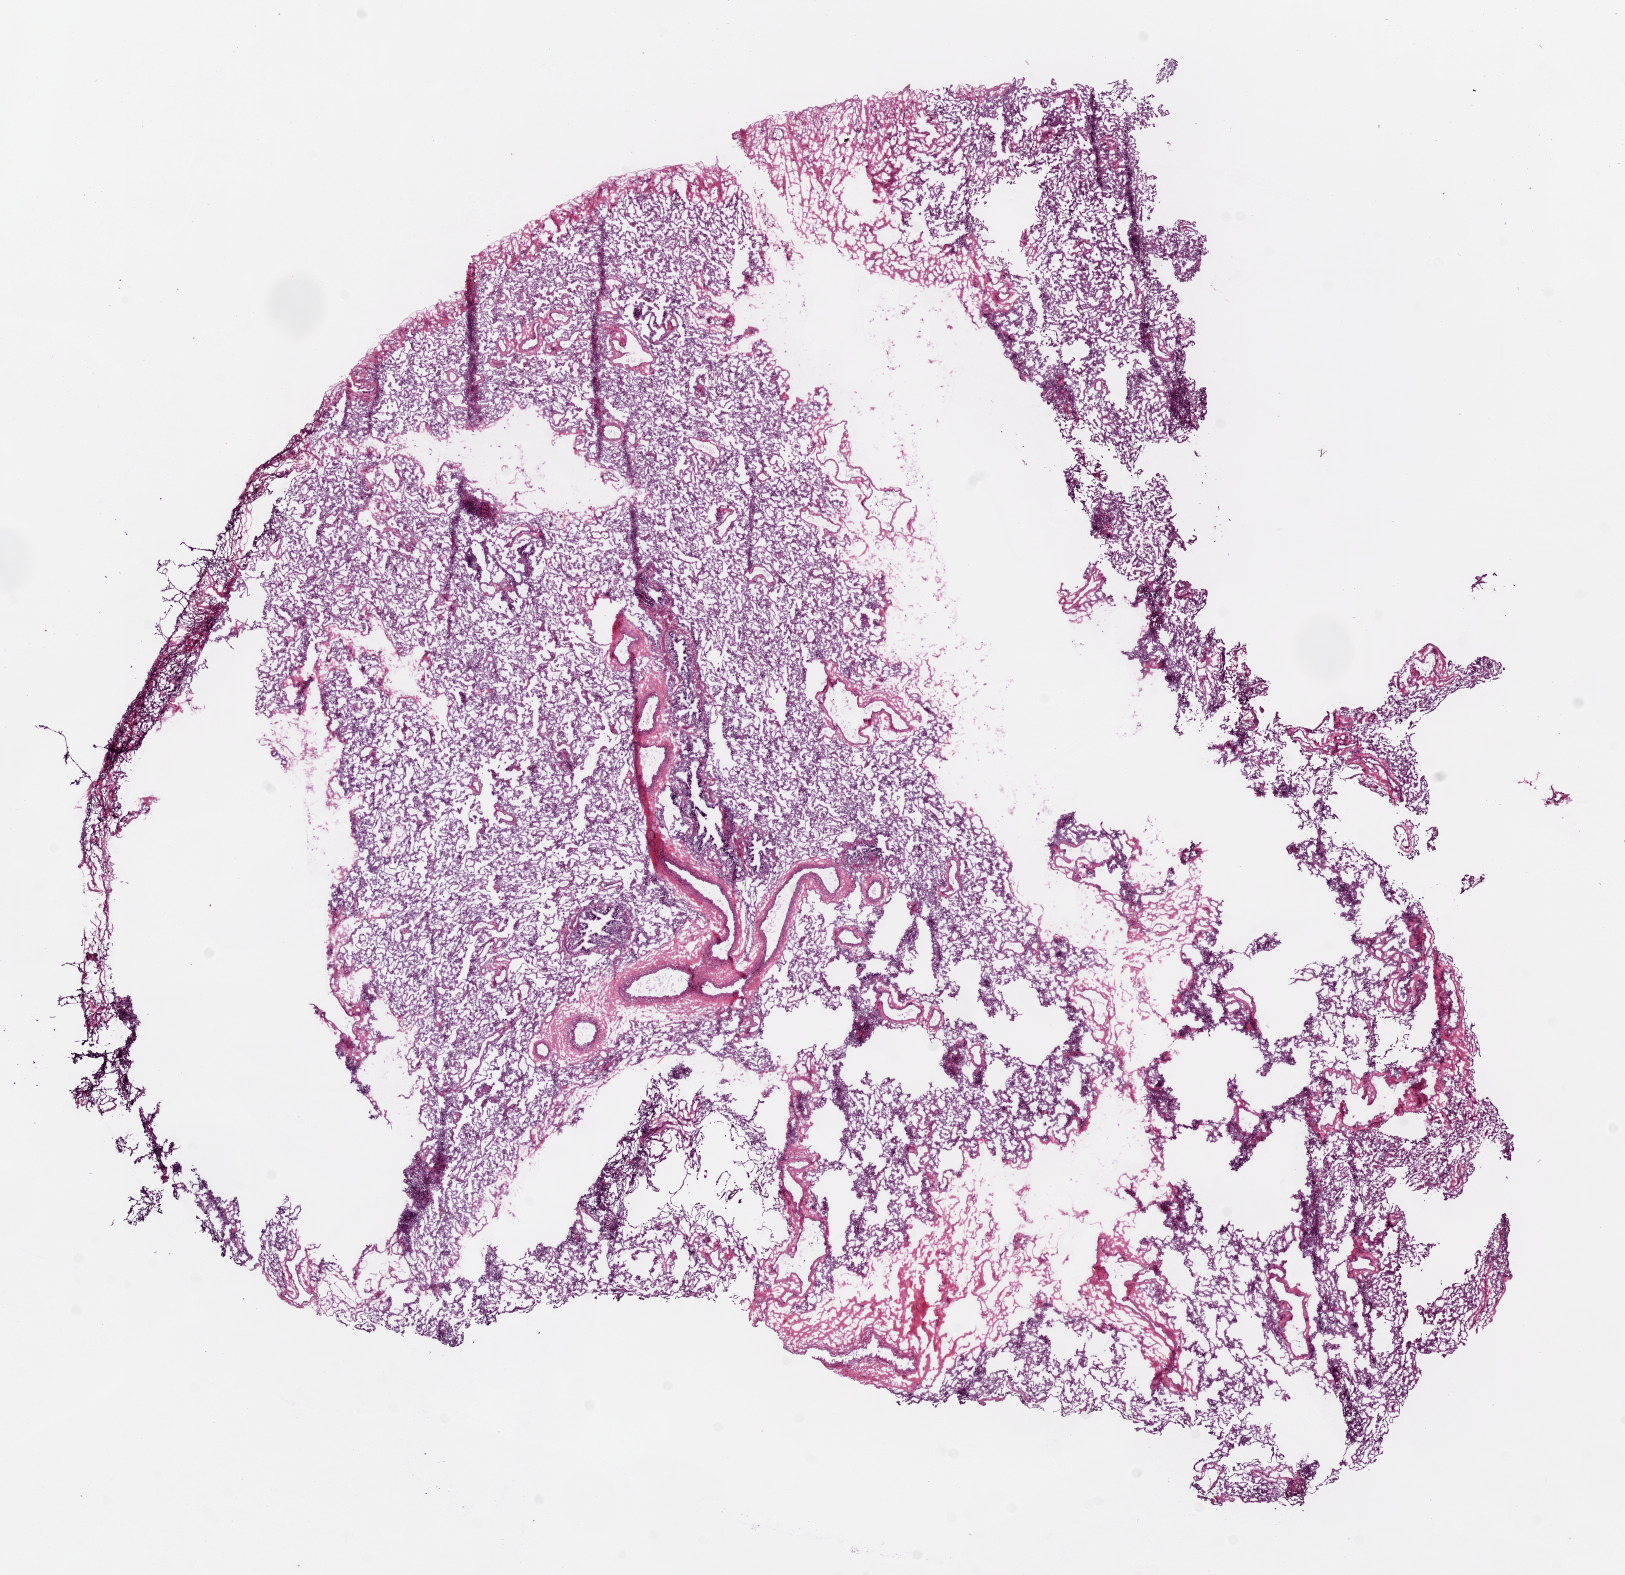
Hematoxylin and eosin (H&E) stained whole-slide image — shown as a low-resolution overview of the whole scanned area (about 13.0 x 12.6 mm, from a 20x scan); frozen section; solid tissue normal (non-tumour tissue) sample from the lung. Patient: female, age at initial diagnosis 51 years.
This section: solid tissue normal (non-tumour) sample from the same patient. Patient diagnosis: Adenocarcinoma, NOS.